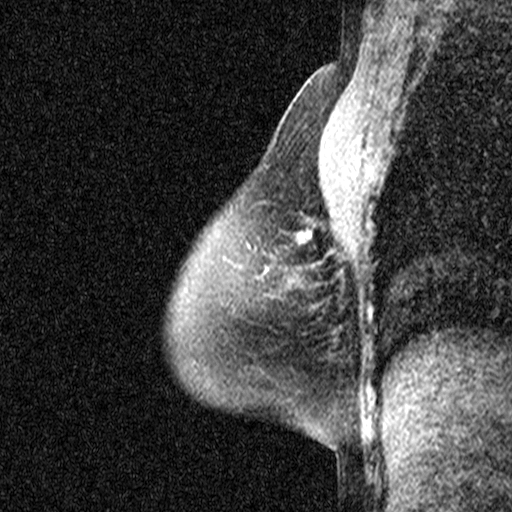
Breast MRI (dynamic contrast-enhanced), one sagittal slice; position 32 of 44 along the scan axis; dynamic contrast-enhanced study with each time point stored as its own series, time point 2 of 3 at this slice position (early post-contrast, ordered by acquisition time); 1.5 T; TE 4.5 ms, TR 11 ms; 512 × 512 image matrix. Female patient, age 54 years. From the clinical record (not read from this slice): setting: breast cancer imaged before/during neoadjuvant chemotherapy; receptor status: HR-positive, HER2-negative.
Structures marked on this image (semi-automatically segmented with operator editing):
- analysis volume of interest (the breast-tissue region the enhancement analysis was run in; not a lesion): bounding box <214,200,333,325> (left, top, right, bottom; pixels)
- tumour enhancement mask (voxels above the 90 % enhancement threshold inside the analysis volume of interest): <299,233,302,236>